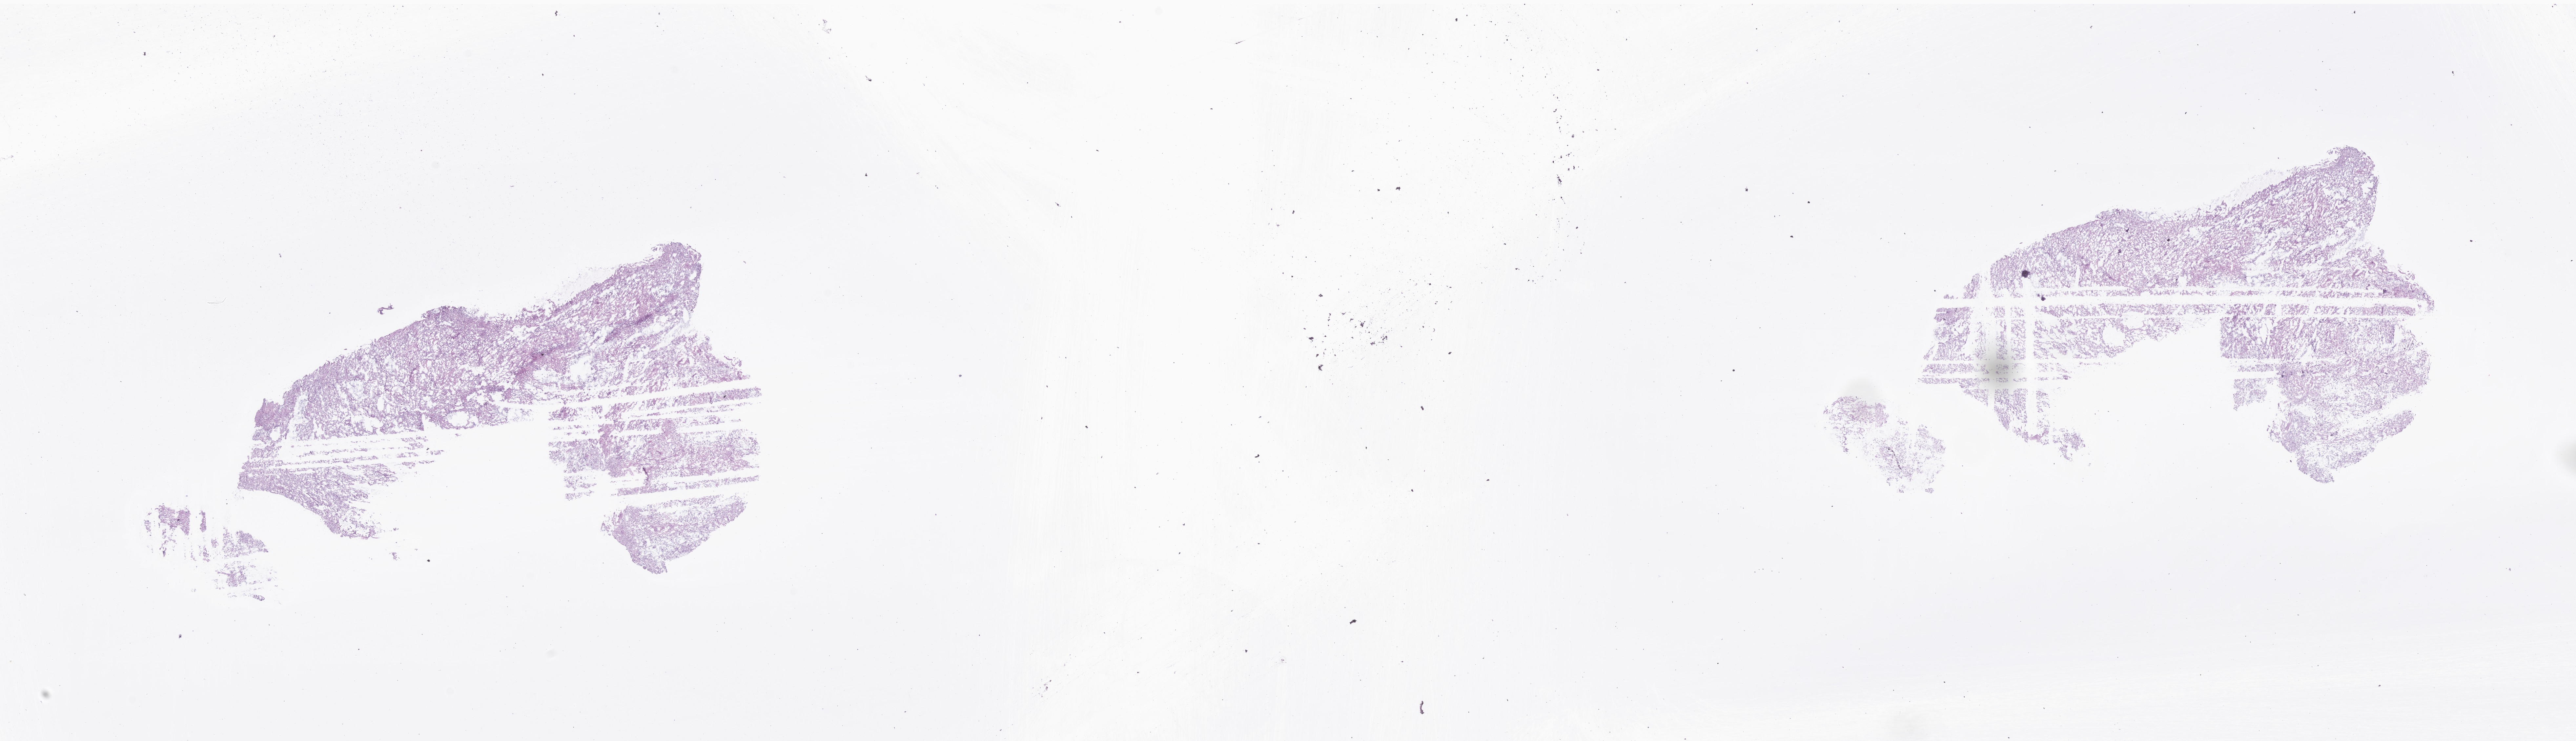
Hematoxylin and eosin (H&E) whole-slide image of tumor tissue from the brain, a low-resolution overview of the entire scanned area, about 33.1 x 9.5 mm. Frozen section. Patient: male, age 199 months.
Diagnosis (ICD-O-3 morphology term): Glioma, malignant.